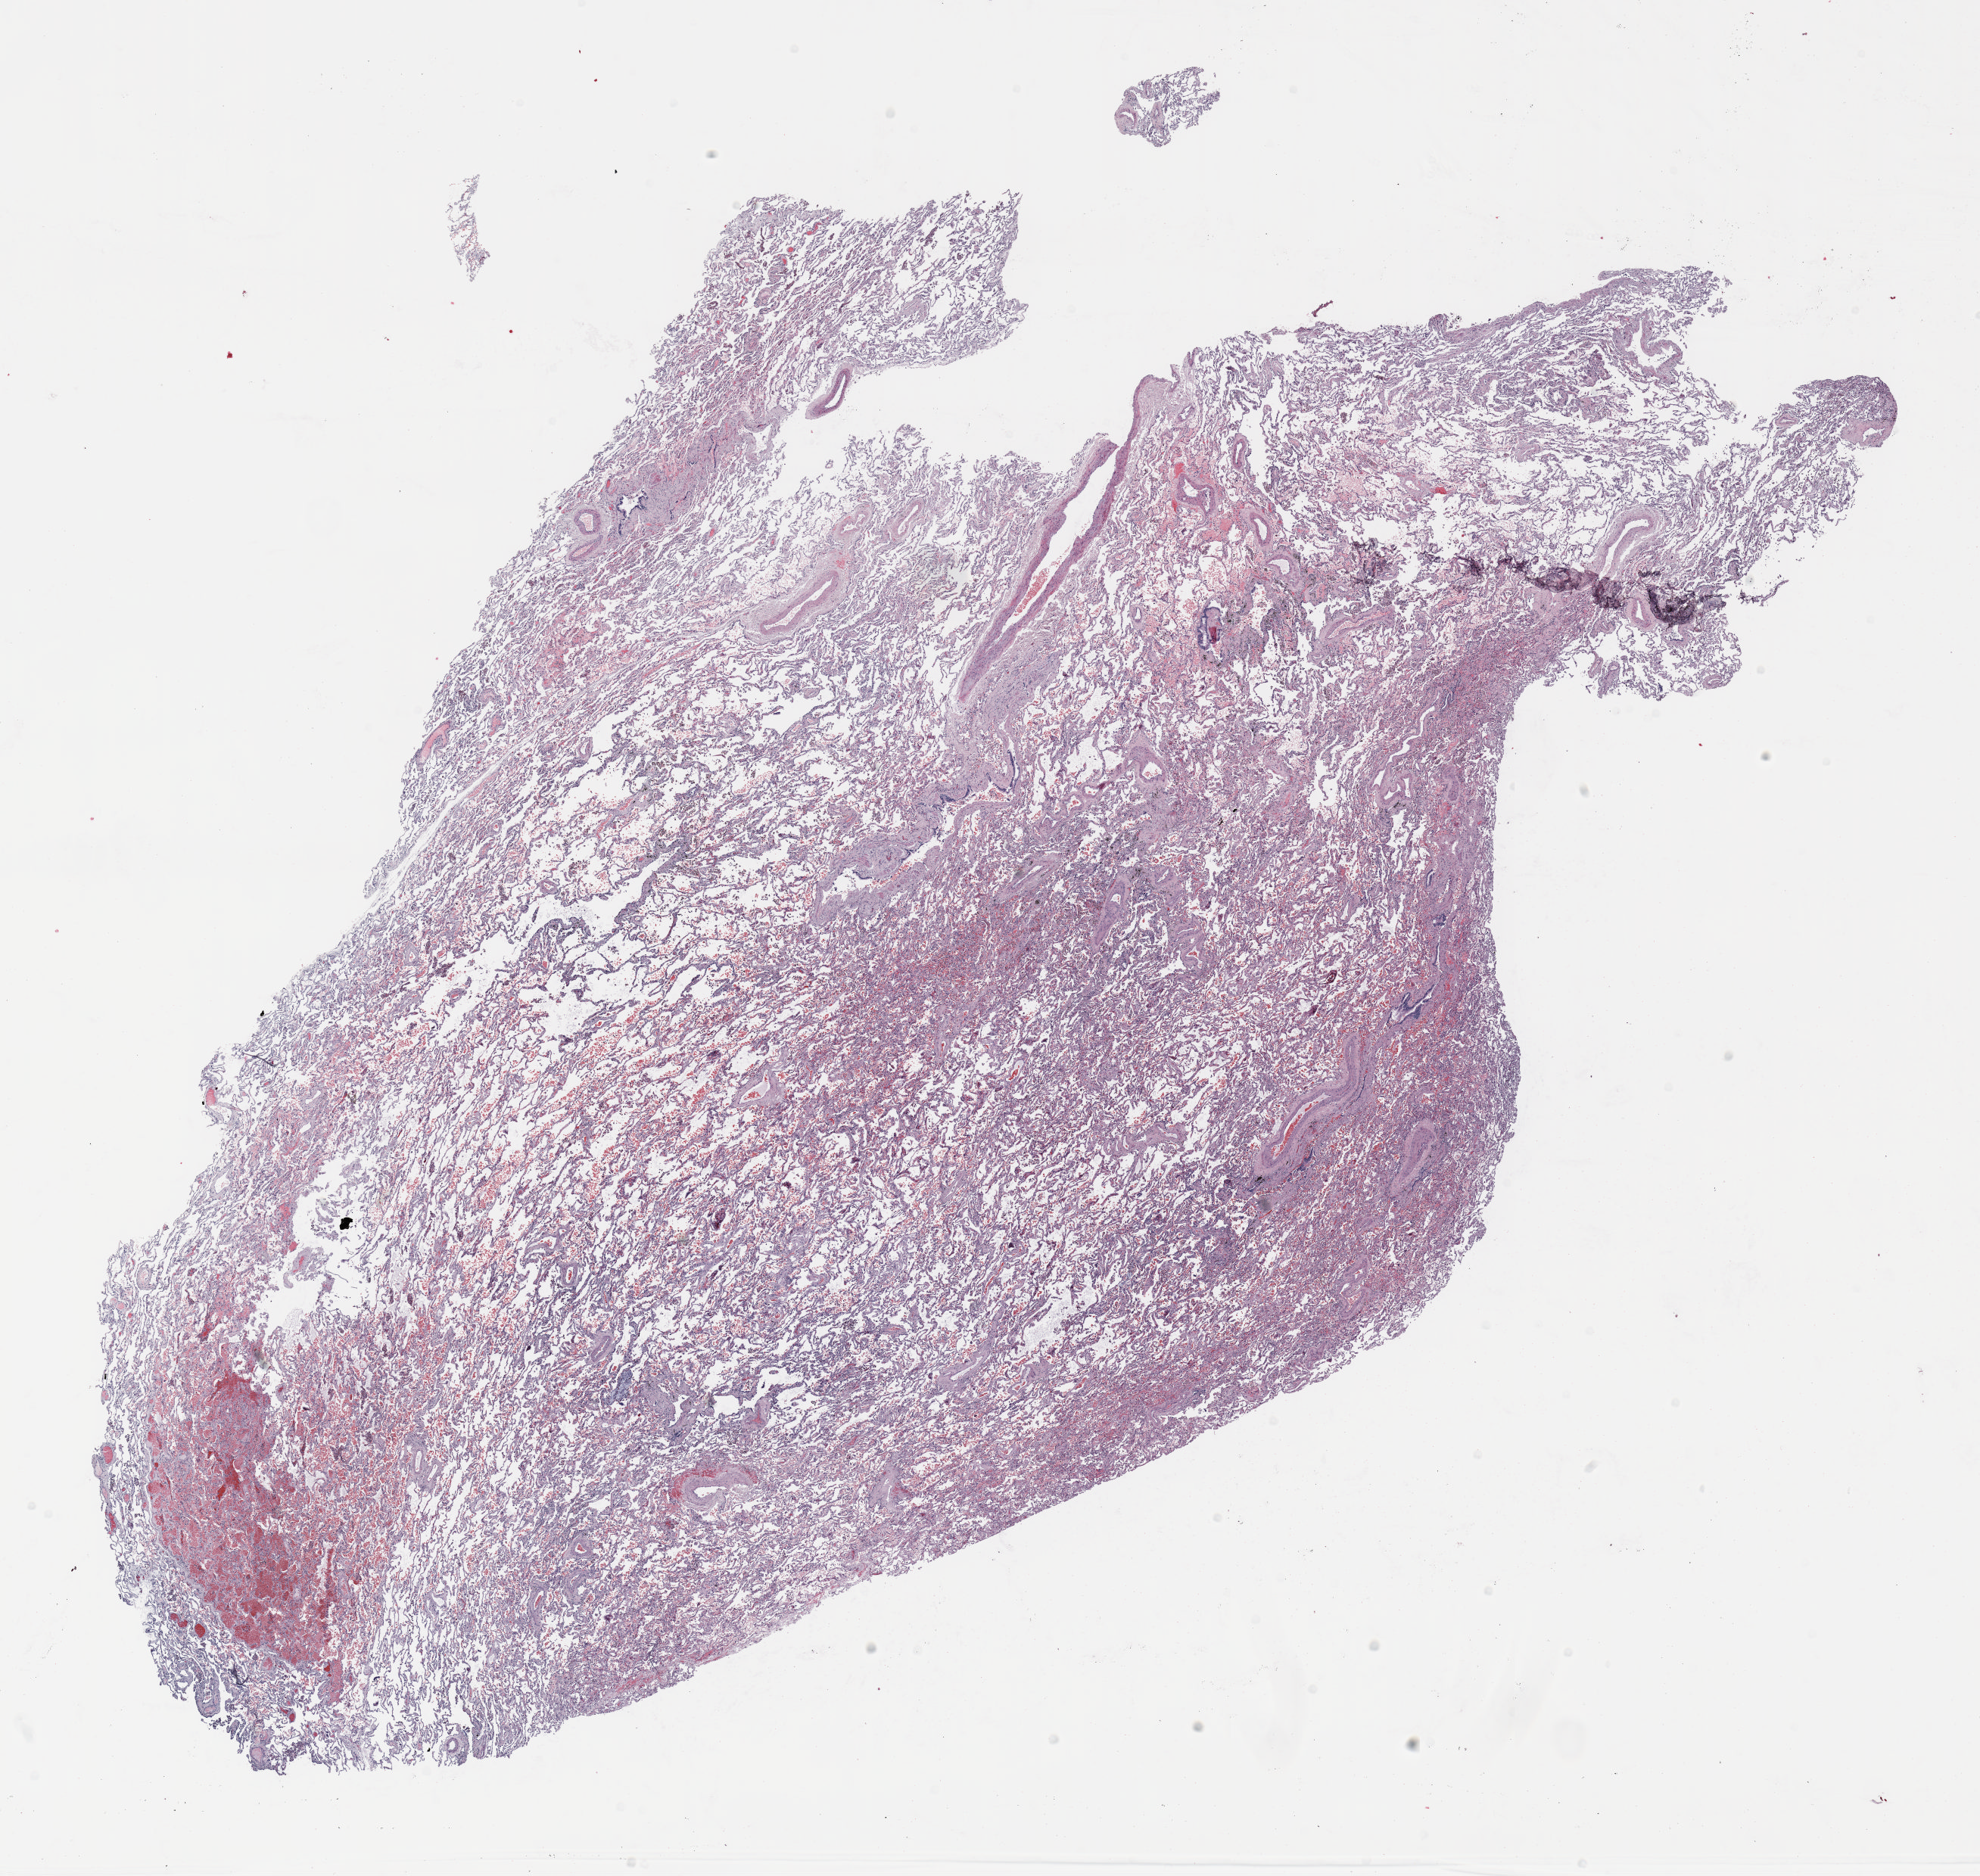
H&E whole-slide image — whole scanned area (about 21.0 x 19.9 mm) shown as a low-resolution overview. FFPE section. Lung. Female patient, aged 57 at enrolment. Current smoker at enrolment. Grade: moderately differentiated (G2).
Participant's lung-cancer diagnosis: Adenocarcinoma, NOS. Tumour size (pathology): 15 mm. Stage (AJCC 6th edition): IA. Primary tumour location (clinical record): right upper lobe.